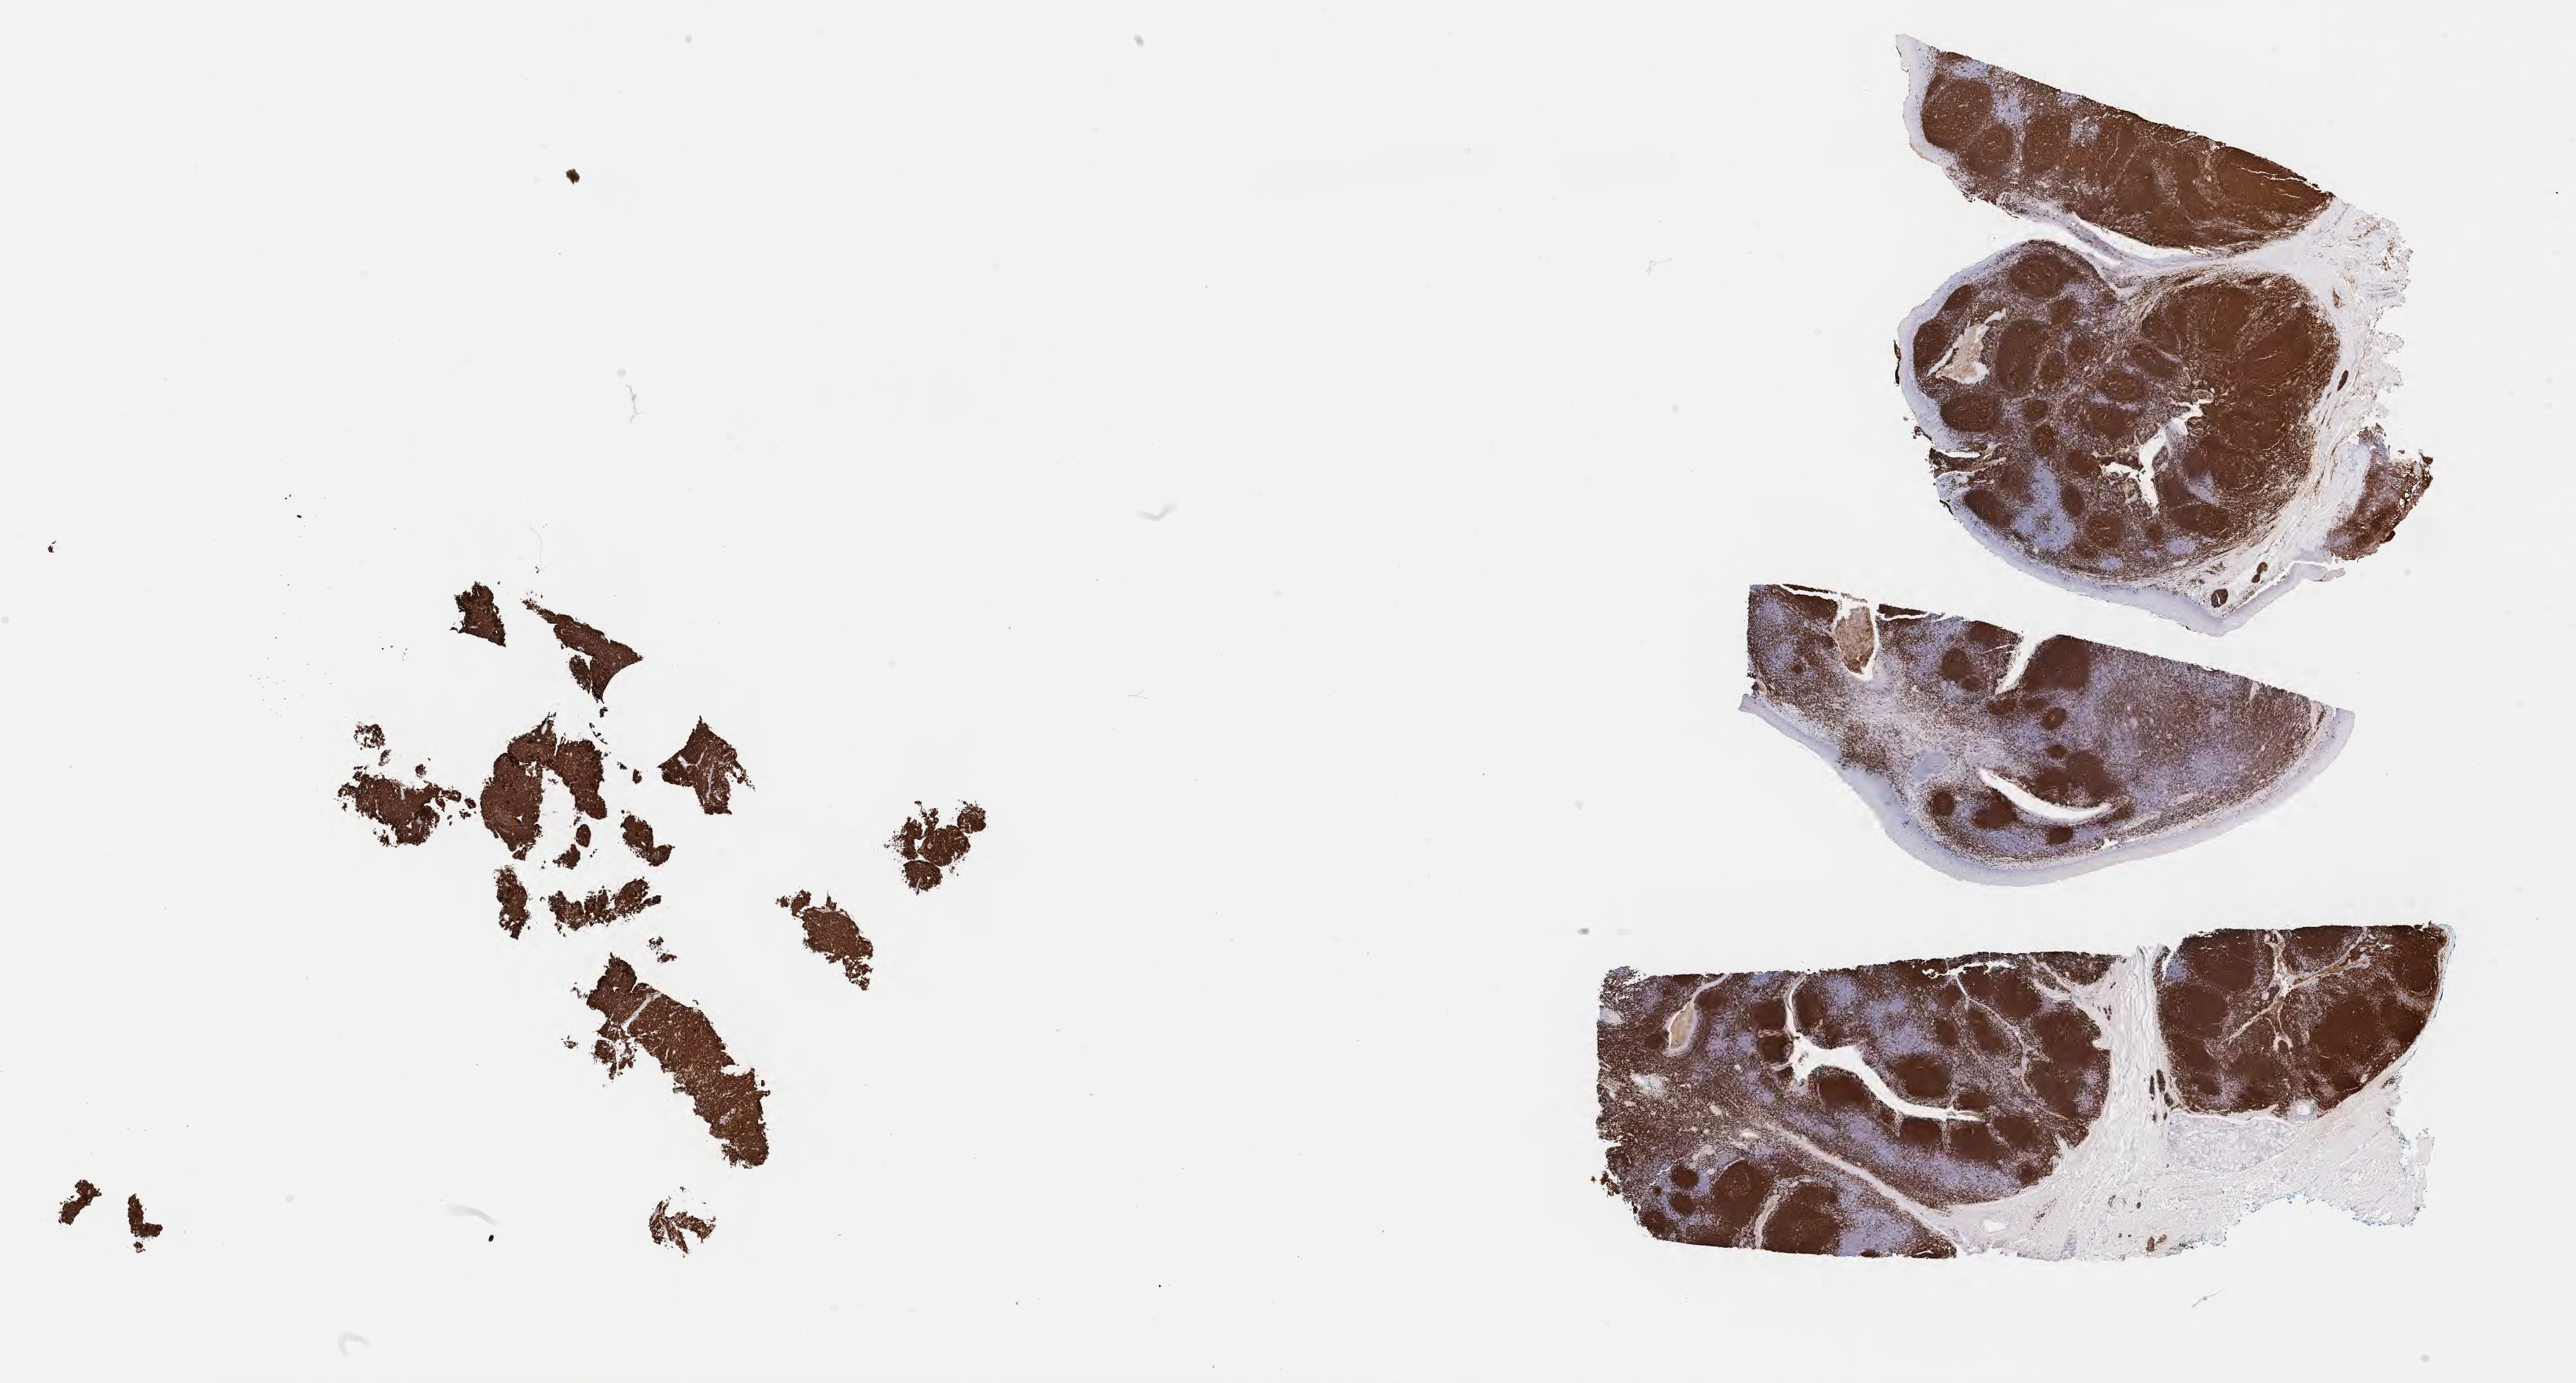
Whole-slide image, immunohistochemical stain for CD20, low-resolution overview of the scanned area, about 30.2 x 16.2 mm. Tumor tissue. Site: kidney. Female, age 8 years at initial diagnosis.
* histologic diagnosis: Burkitt lymphoma, NOS